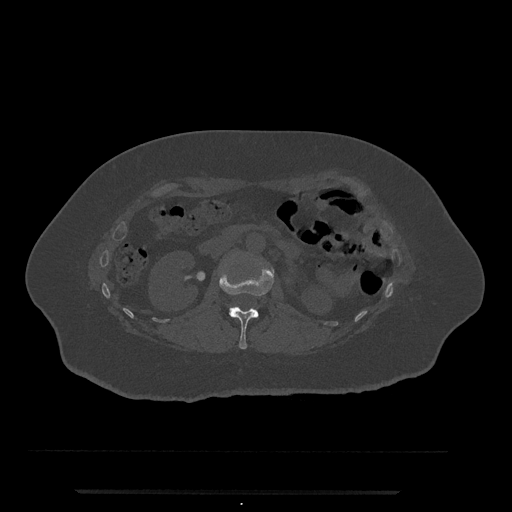
CT including the spine, one axial slice. Slice 86 of 797 in the series (ordered by position). 120 kVp. Bone window (W 1800 / L 400 HU). 0.5 mm slice thickness. 512 × 512 image matrix, field of view 440 × 440 mm. Patient: female, 51 years. From the clinical record (not read from this slice): primary cancer: neuro; vertebrae with lytic lesions (as recorded): T8.
Structures marked on this image (semi-automatic segmentation, software-assisted and operator-edited):
- L1 vertebra: bounding box [x1, y1, x2, y2] px = [219, 266, 274, 350]
- L2 vertebra: [229, 306, 237, 311]